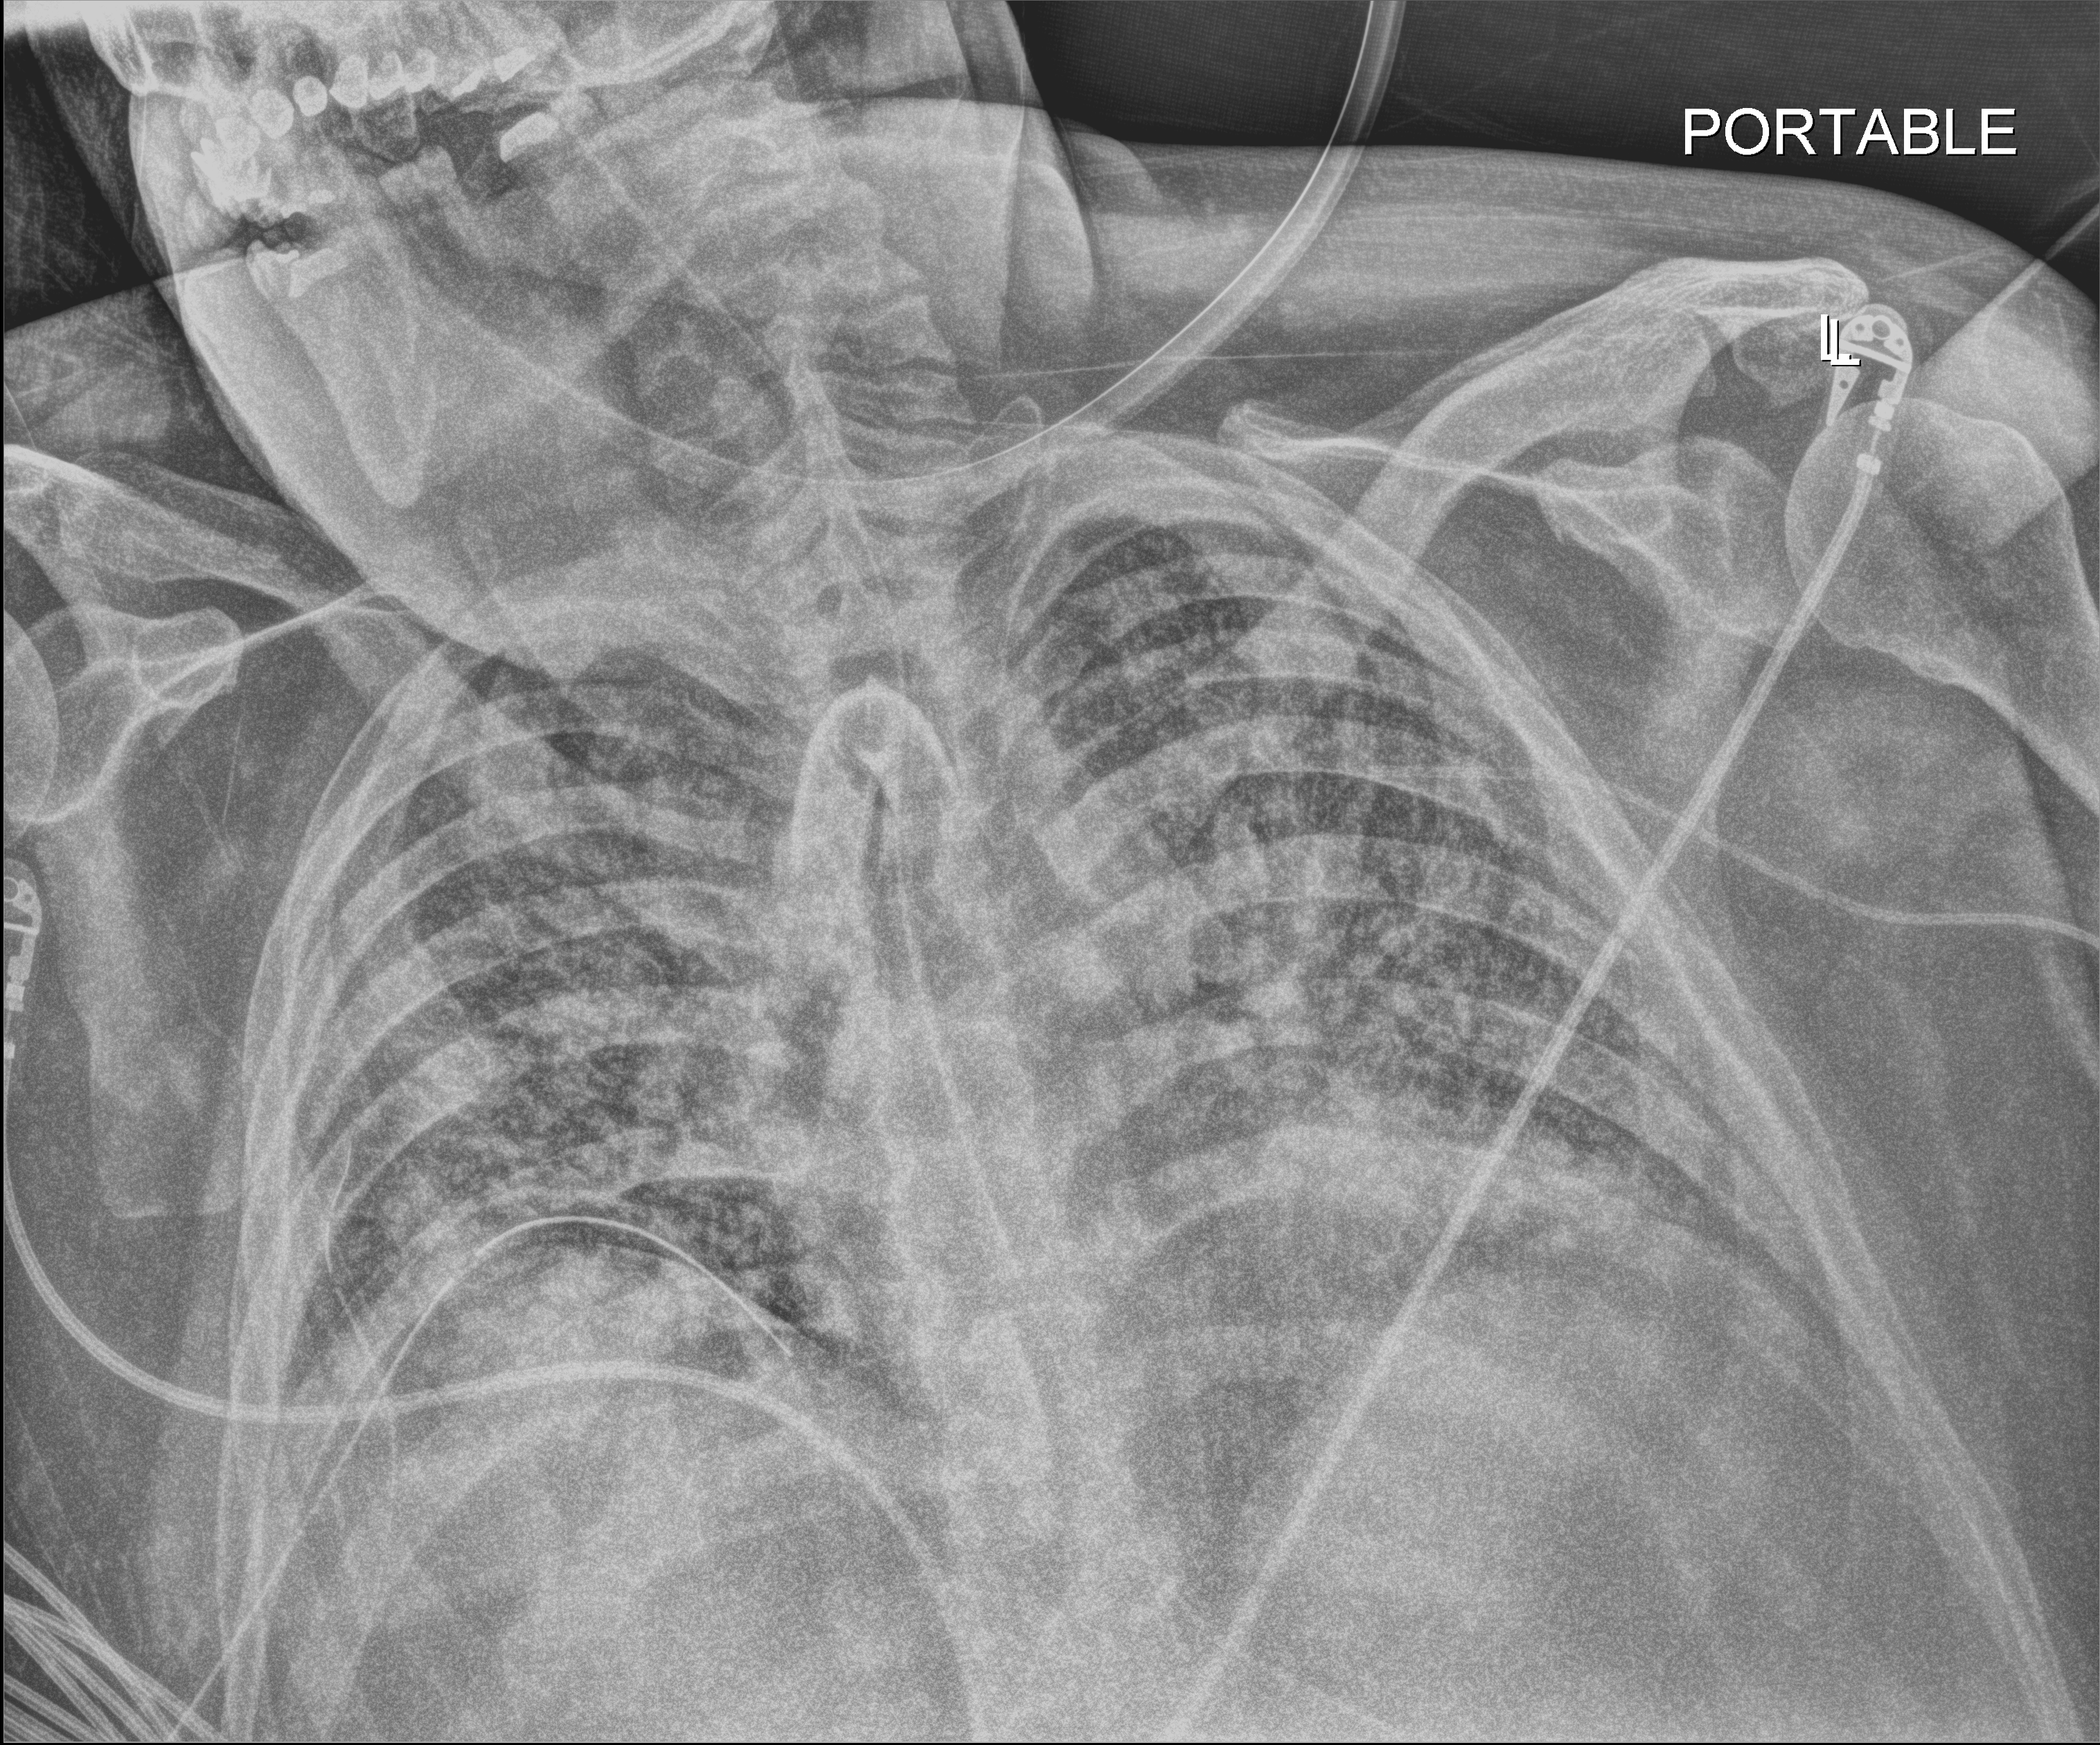
Chest radiograph (digital radiography), anteroposterior (AP) projection. Patient hospitalised with COVID-19; male, aged 18–59 years.
From the hospital-stay record, not from the radiograph (when in the stay this image was taken is not recorded):
- mechanically ventilated during this hospital stay: yes
- admitted to intensive care during this hospital stay: yes
- other chronic lung disease (admission record): no